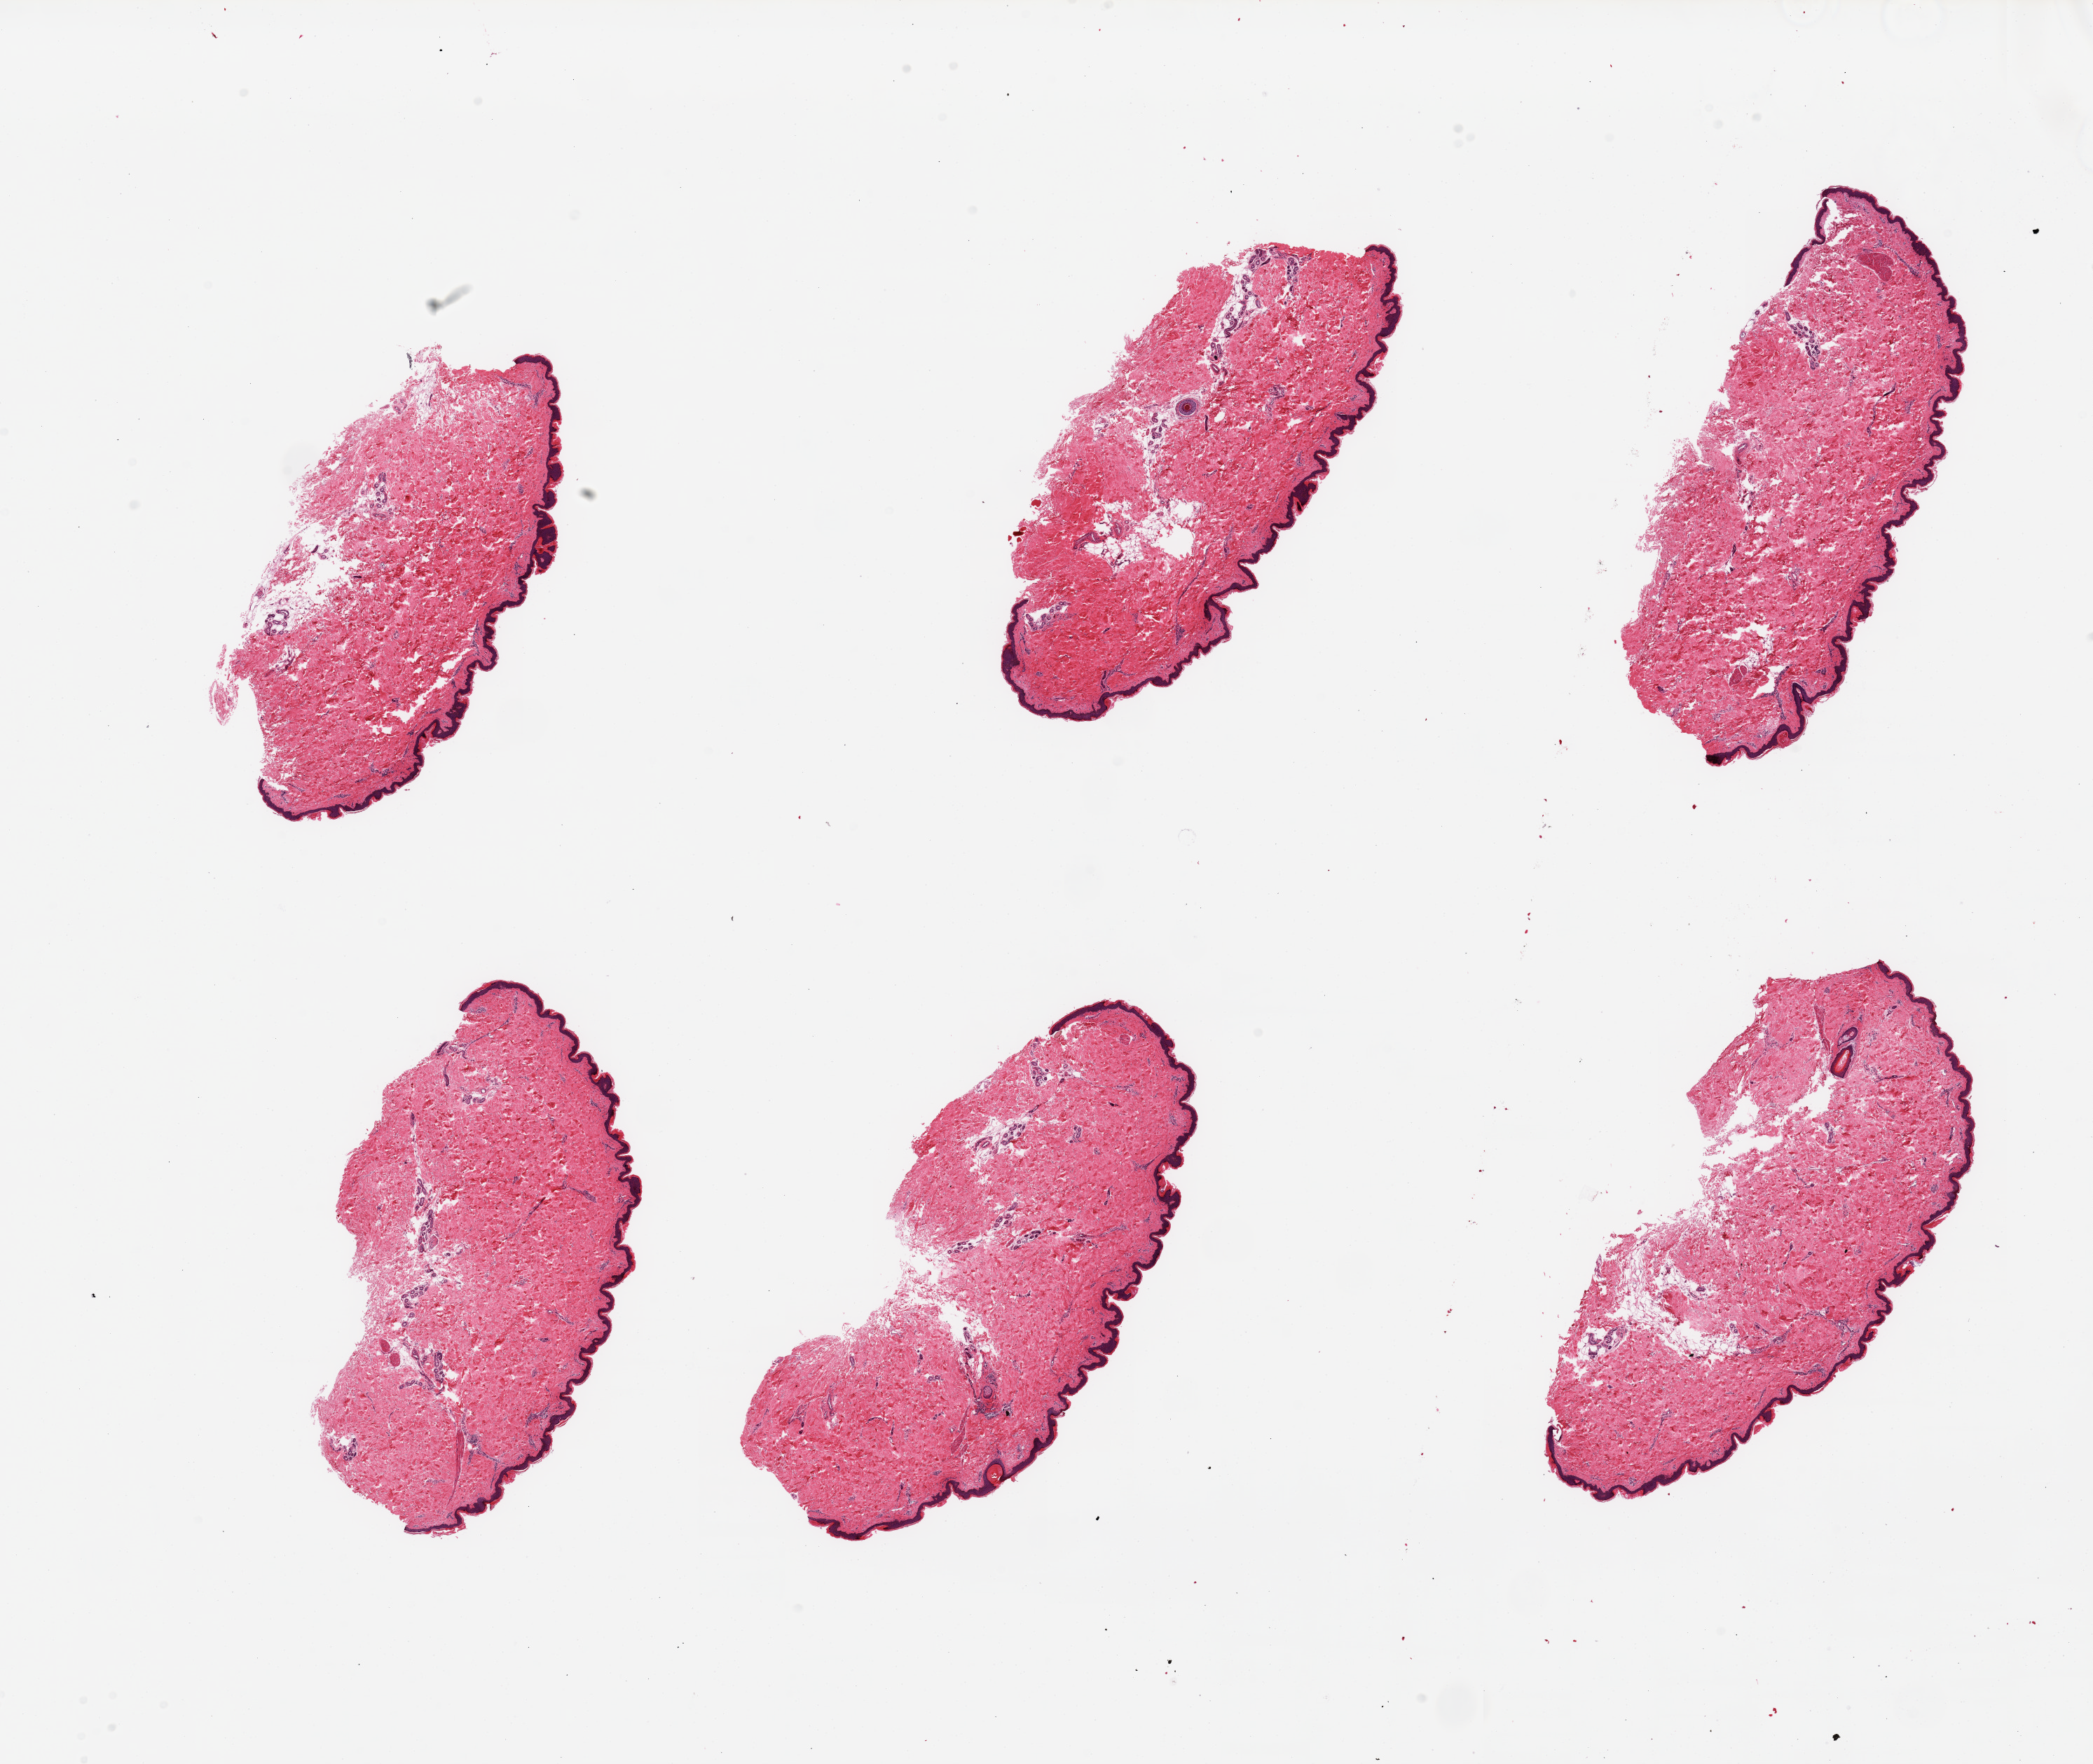
Whole-slide image, H&E stain, brightfield — shown as a low-resolution overview of the whole scanned area (about 23.6 x 19.9 mm); PAXgene-fixed paraffin-embedded (PFPE) section; section of skin of lower leg (target tissue); donor tissue sample. Donor sex: male.
* review note (as recorded): 6 pieces; well trimmed skin with mostly periadnexal fat; 43 micron thick epidermis